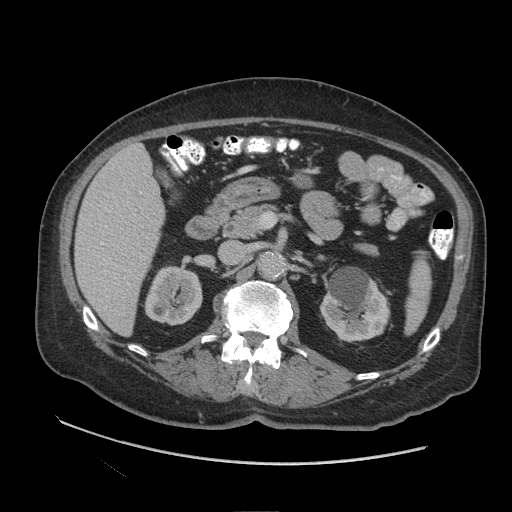
Contrast-enhanced abdominal CT (liver protocol), one axial slice; position 43 of 109 along the scan axis; reconstruction kernel STANDARD; soft-tissue window (W 400 / L 40 HU); 2.5 mm slice thickness; 512 × 512 image matrix. Case-level facts recorded for this patient, not image findings: diagnosis: hepatocellular carcinoma (patient treated with transarterial chemoembolisation; whether this scan precedes or follows treatment is not stated here); TNM stage (as recorded): Stage-I; Child-Pugh class: A.
Outlined on this slice (semi-automatically segmented with operator editing):
- liver parenchyma outside the tumour (the mass and vessels are separate outlines, so this box may not span the whole liver): bounding box <74,144,164,334> (left, top, right, bottom; pixels)
- liver vessels: <98,192,142,285>